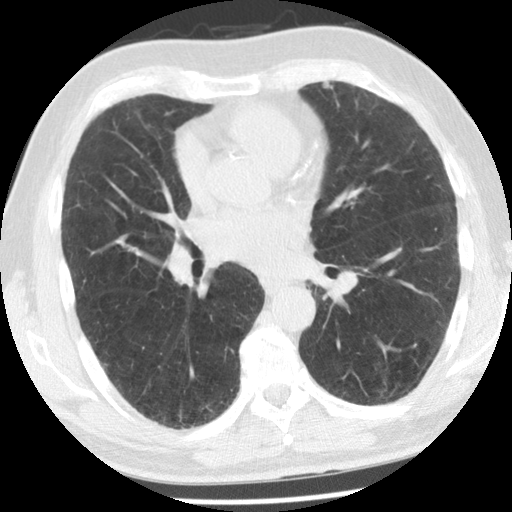
Chest CT (low-dose screening protocol), one axial image; first (baseline) screen; lung window (W 1500 / L -600 HU); 2.5 mm slice thickness; 140 kVp; slice 68 of 131 in the series. Male, age 66 years at enrolment. Former smoker at enrolment.
• Expert-annotated lung lesion, bounding box (x1, y1, x2, y2) in pixels: (307, 71, 348, 107).
• The exam's reader record, not a measurement of the box and not confirmed to be the same lesion: non-calcified nodule or mass ≥4 mm, lingula, 5 × 4 mm, smooth margins, soft tissue attenuation.
• Later outcome: lung cancer diagnosed 449 days after this screen (after the second annual screen) — adenocarcinoma, NOS, left upper lobe, moderately differentiated (G2), stage IIB (AJCC 6th edition), 9 mm at pathology.